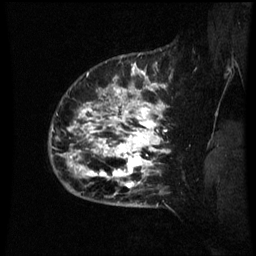
Breast MRI (dynamic contrast-enhanced), one sagittal slice. Position 54 of 60 along the scan axis. Dynamic contrast-enhanced series, image 2 of 3 at this slice position (ordered by acquisition). 1.5 T. TE 4.2 ms, TR 8.9 ms. 256 × 256 image matrix, field of view 200 × 200 mm. Patient: female, 42 years. Case-level facts recorded for this patient, not image findings: setting: breast cancer imaged before/during neoadjuvant chemotherapy; receptor status: HER2-positive.
Outlined on this slice (semi-automatically segmented with operator editing):
- analysis volume of interest (the breast-tissue region the enhancement analysis was run in; not a lesion): bounding box <66,82,171,193> (left, top, right, bottom; pixels)
- tumour enhancement mask (voxels above the 70 % enhancement threshold inside the analysis volume of interest): <66,84,169,187>